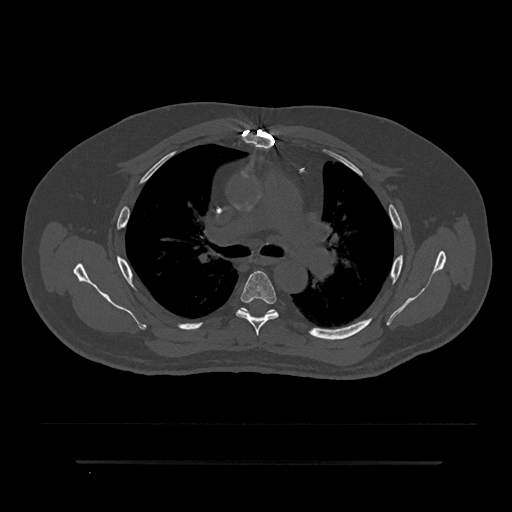
CT including the spine, one axial slice. Position 566 of 797 along the scan axis. Reconstruction kernel Br40s/3. Bone window (W 1800 / L 400 HU). 0.5 mm slice thickness. 512 × 512 image matrix. Male patient, age 59 years. Case-level facts recorded for this patient, not image findings: primary cancer: bile ducts.
Outlined on this slice (semi-automatic segmentation, software-assisted and operator-edited):
- T5 vertebra: box from (x=236, y=271) to (x=279, y=336) px
- T6 vertebra: (x=239, y=308)–(x=274, y=314)